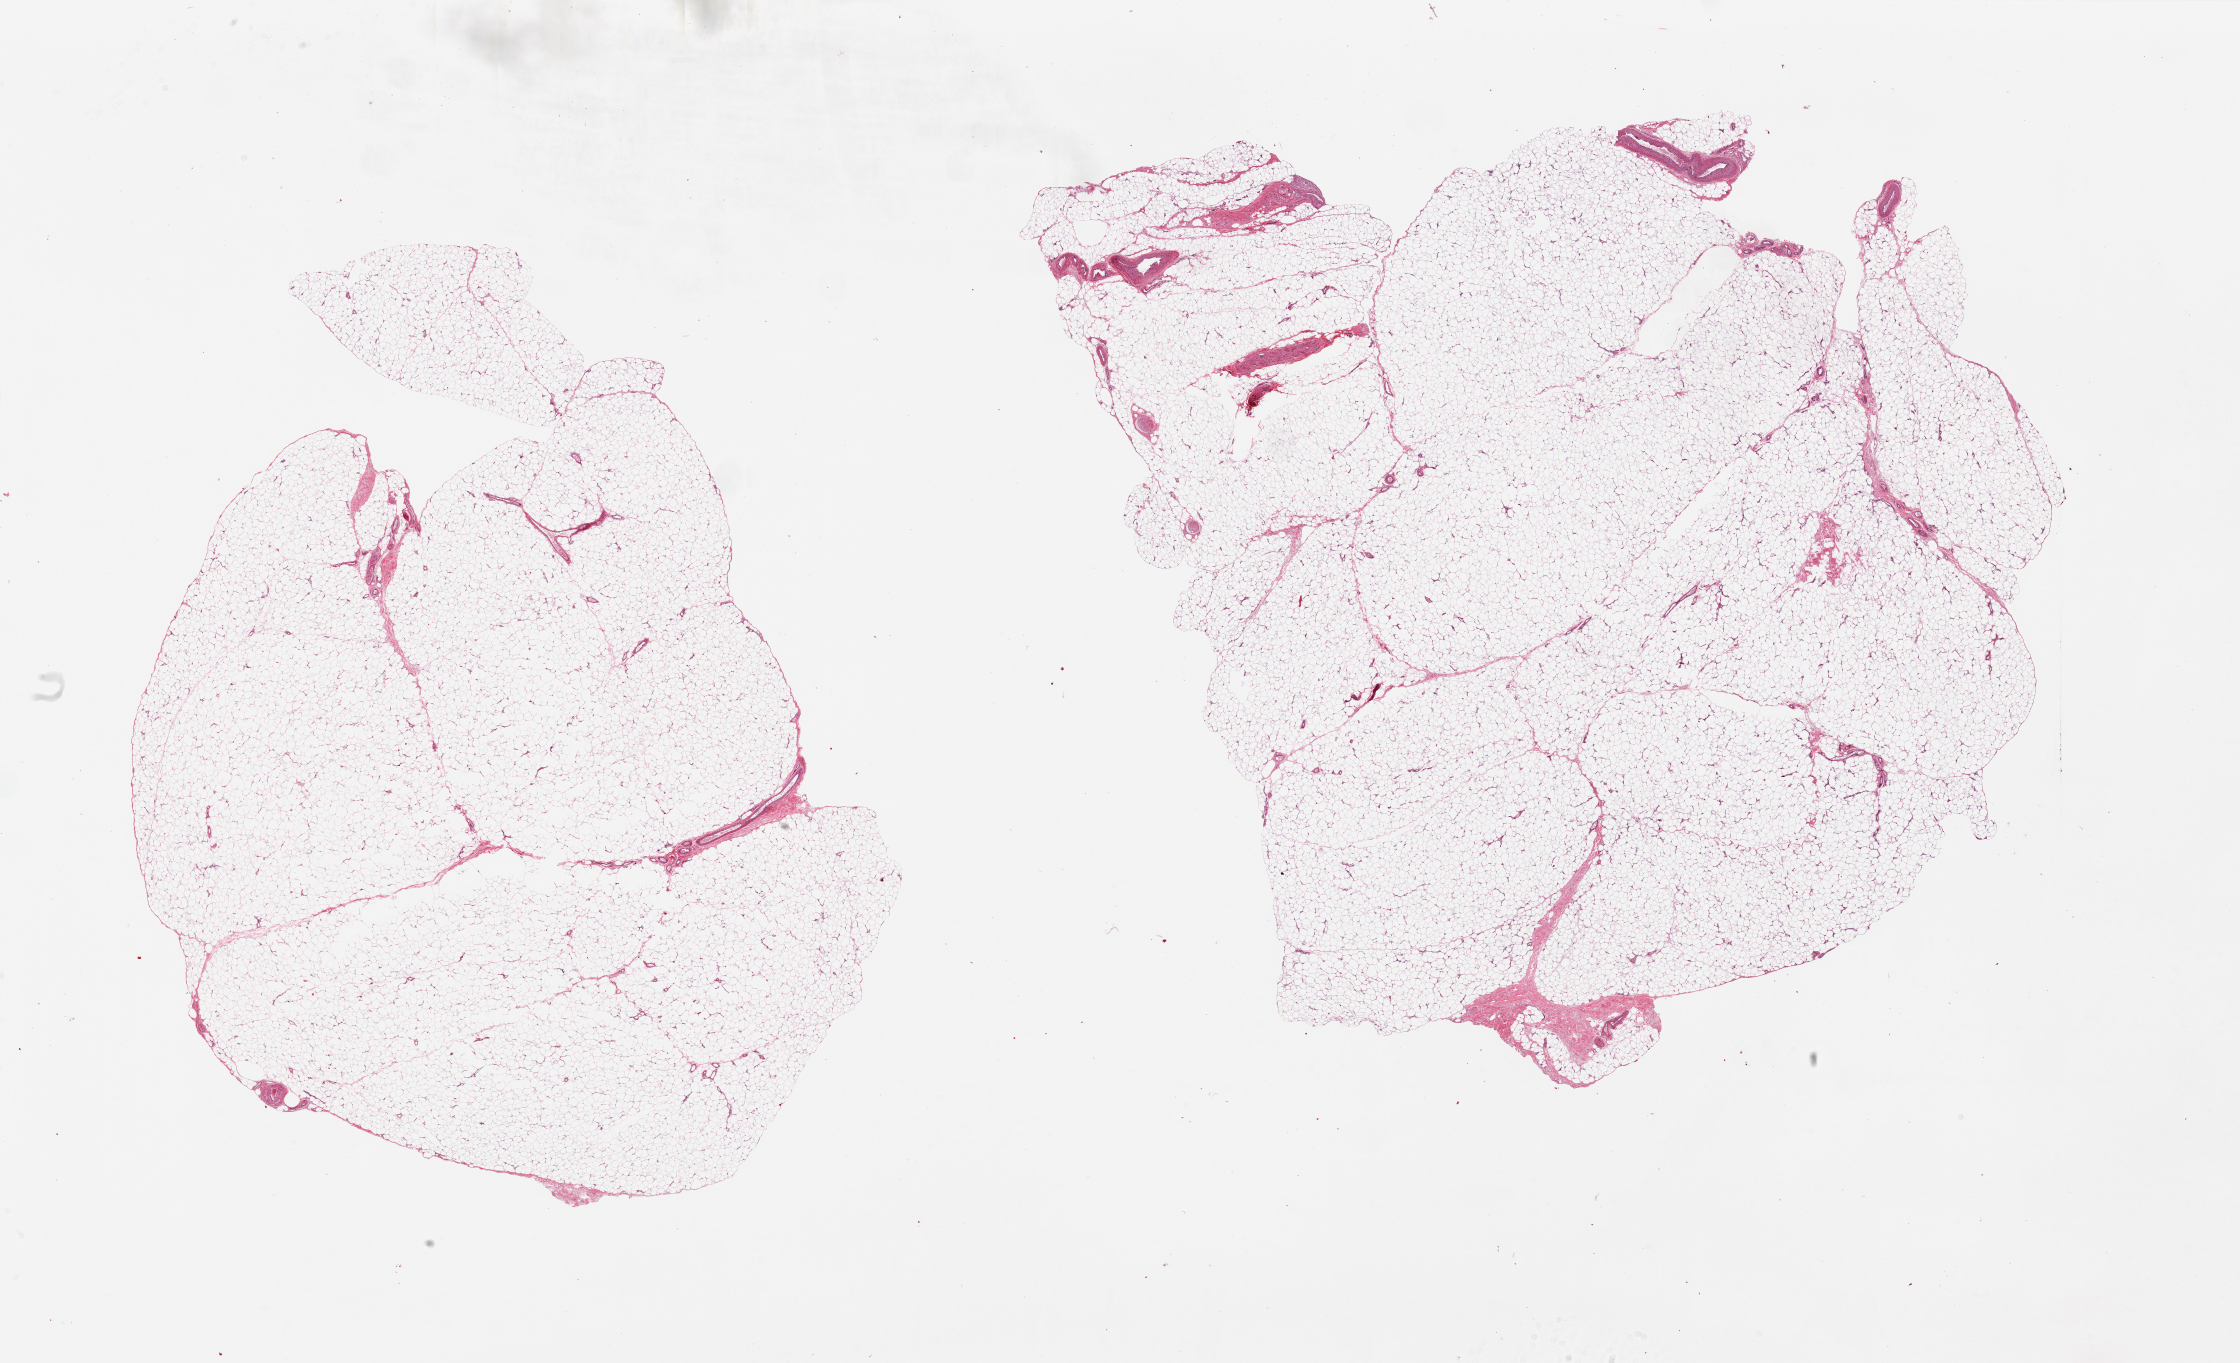
Digitized haematoxylin and eosin-stained section, whole scanned area (about 35.4 x 21.6 mm, slide scanned at 20x) shown as a low-resolution overview, PAXgene-fixed paraffin-embedded (PFPE) section, section of adipose tissue (target tissue), tissue donor sample. Male donor.
Pathologist's review note for this sample: 2 pieces.